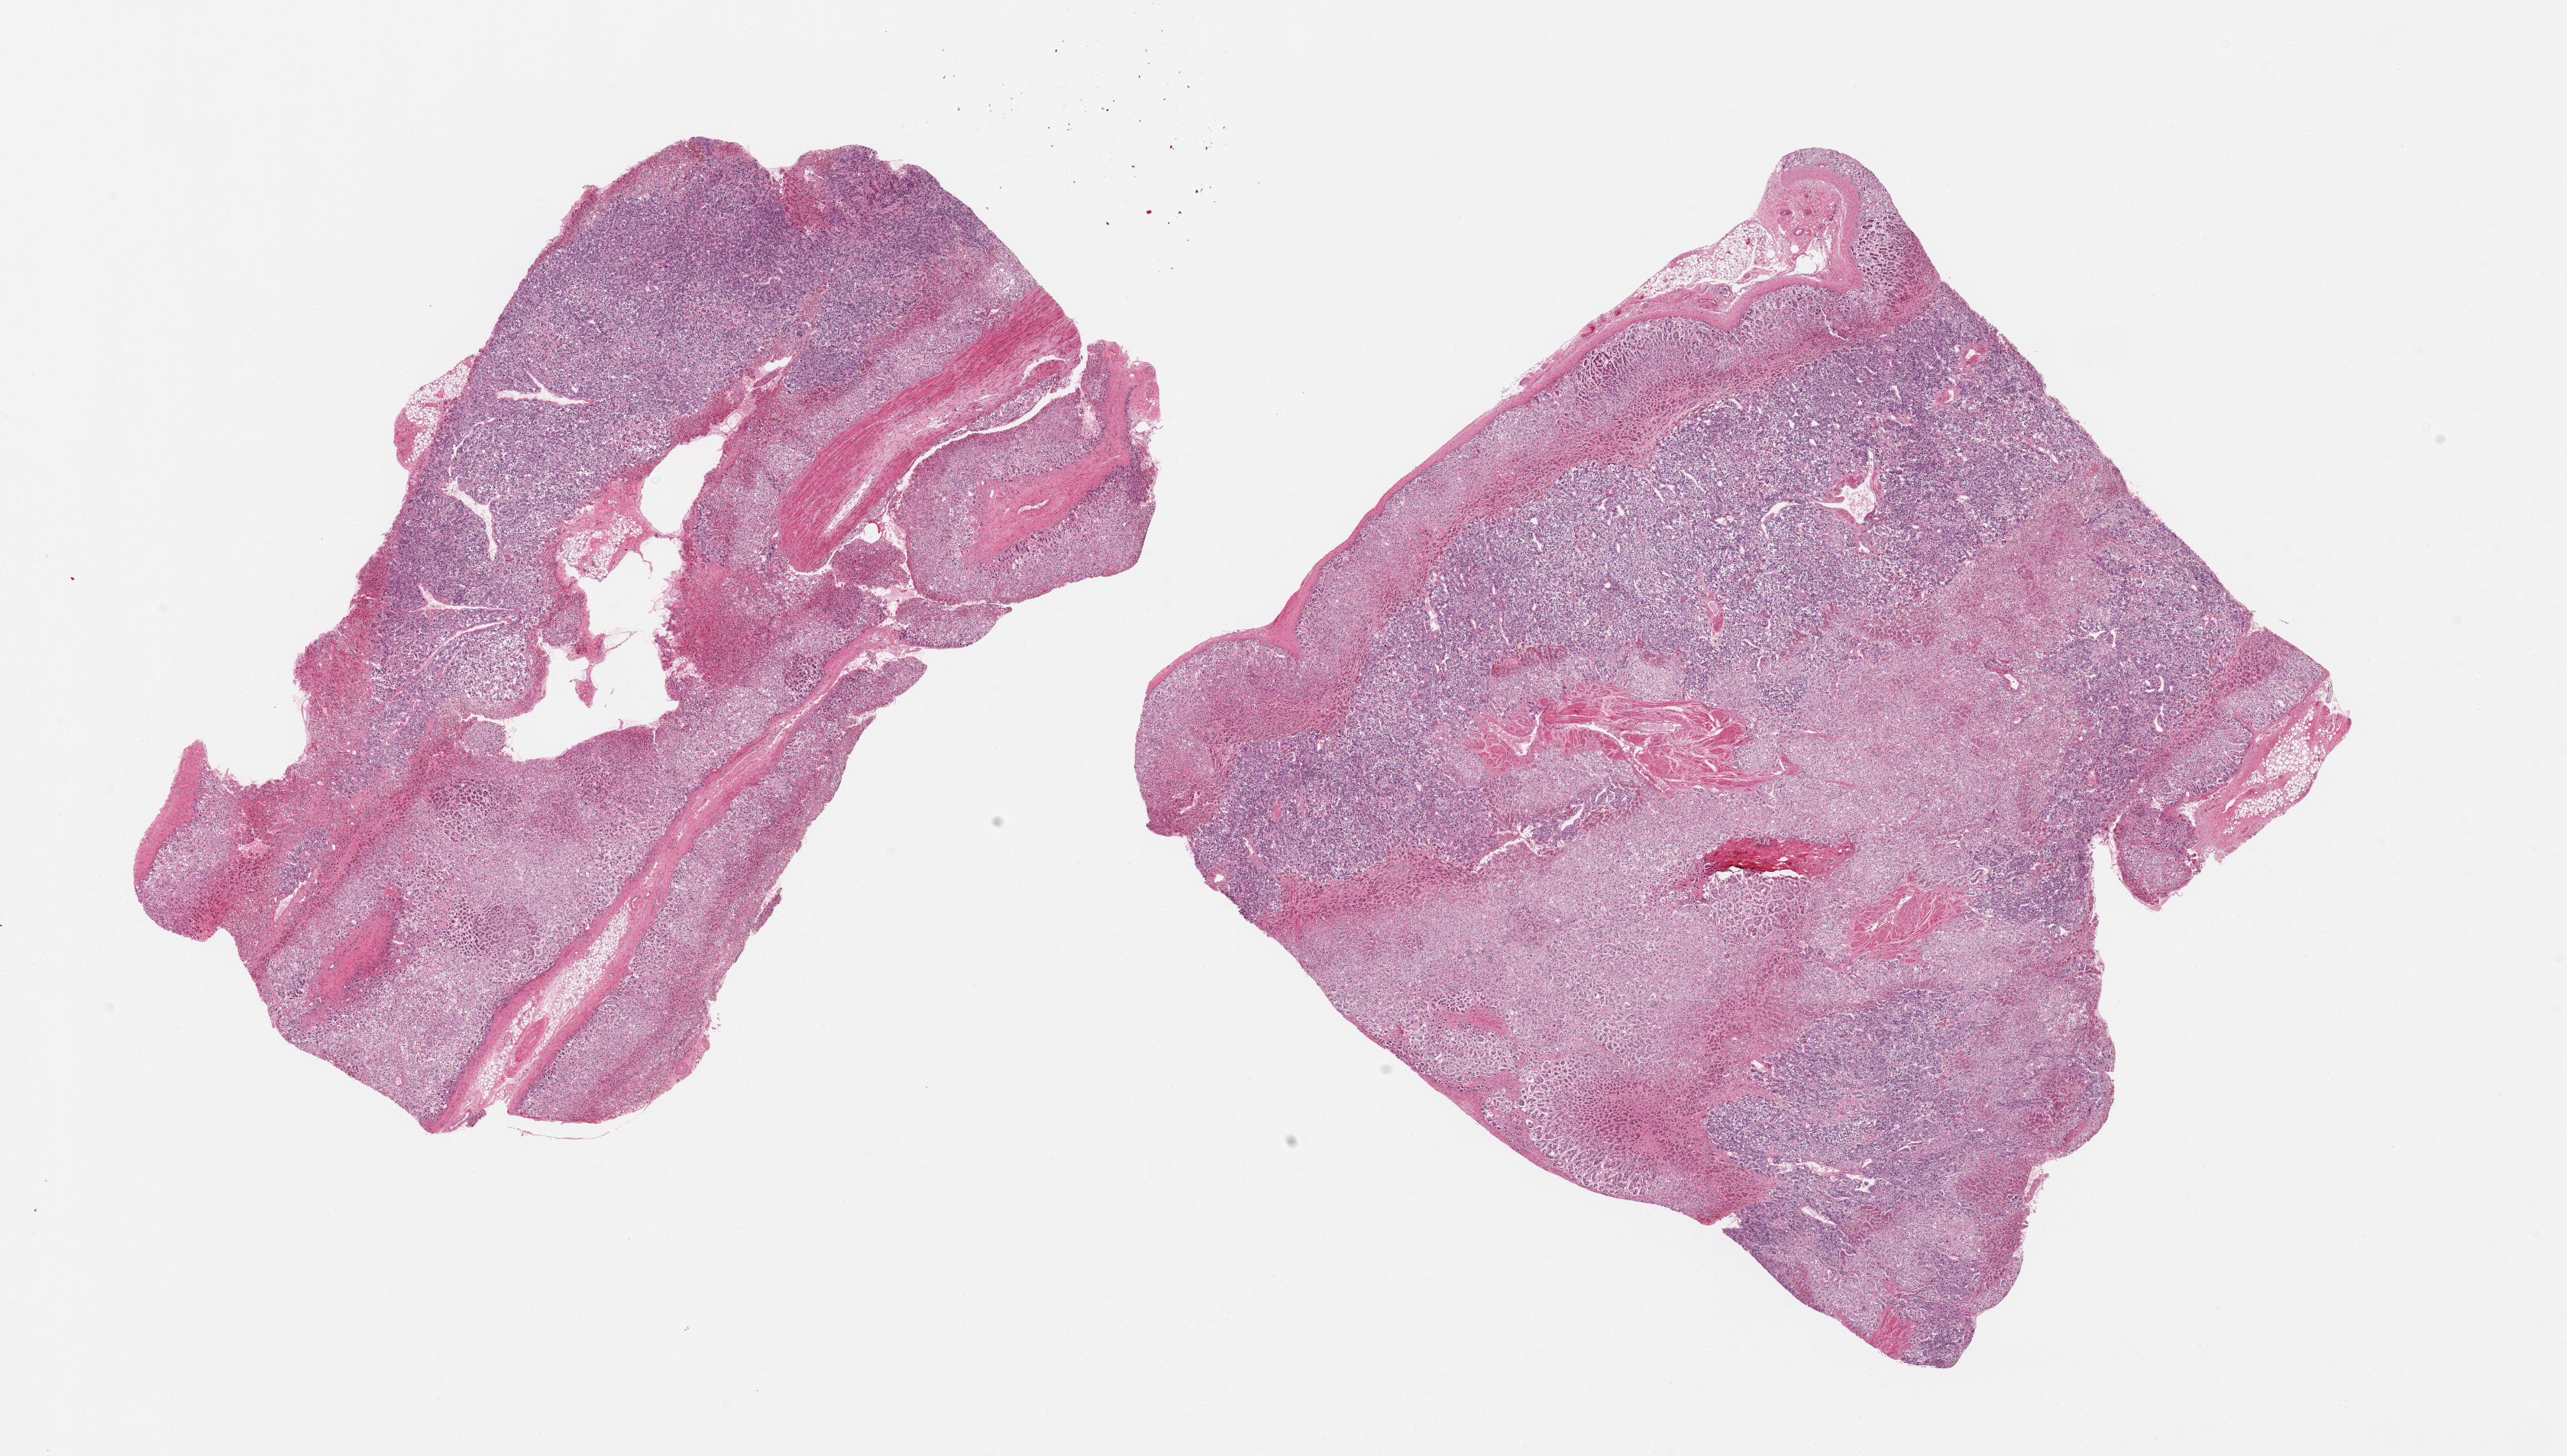
Whole-slide image, hematoxylin and eosin (H&E) stain — a low-resolution overview of the entire scanned area, about 26.6 x 15.1 mm (slide scanned at 20x), PAXgene-fixed, paraffin-embedded tissue, section of adrenal gland (target tissue), donor tissue sample.
• review note (as recorded): 2 pieces, cortex, advanced autolysis